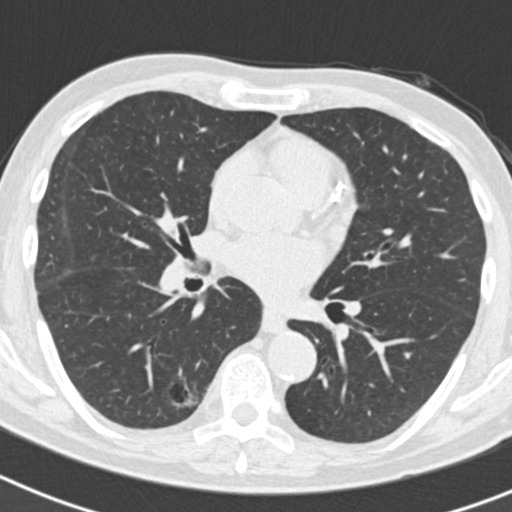
Axial slice from a low-dose chest CT screening exam. Second annual screen. Lung window (W 1500 / L -600 HU). Standard (soft-tissue) reconstruction kernel (B30f). 120 kVp. Slice 87 of 186 in the series. 512 × 512 image matrix. Male, age 70 years at enrolment. Current smoker at enrolment.
Expert-annotated lung lesion, box from (x=128, y=366) to (x=203, y=431) px. The screening reader recorded 5 non-calcified nodules or masses ≥4 mm on this exam (right lower lobe, right lower lobe, right upper lobe, right upper lobe, left upper lobe); which of them this box marks is not recorded. Participant outcome: lung cancer diagnosed 622 days after this screen (after the third annual screen) — bronchiolo-alveolar adenocarcinoma, NOS, right lower lobe, poorly differentiated (G3), stage IB (AJCC 6th edition), 30 mm at pathology.